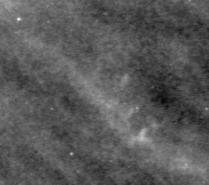
Crop from a digitized film mammogram around one marked abnormality; right breast; MLO view.
- Calcifications, morphology pleomorphic, distribution clustered; BI-RADS assessment category 4; pathology (as recorded): benign.